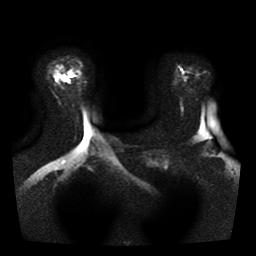
Breast MRI, one axial slice; position 29 of 41 along the scan axis; diffusion-weighted series; image 2 of 4 stored at this slice position (different b-values; order by instance number); 1.5 T; 5 mm slice thickness; 256 × 256 image matrix, field of view 330 × 330 mm. Female patient.
Annotated regions visible in this slice (expert manual segmentation):
- tumour on diffusion-weighted imaging: box from (x=61, y=75) to (x=66, y=79) px